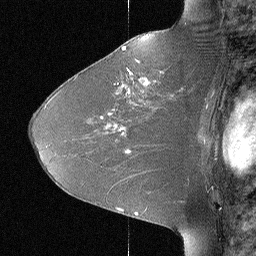
Breast MRI (dynamic contrast-enhanced), one sagittal slice; position 41 of 64 along the scan axis; dynamic contrast-enhanced study with each time point stored as its own series, time point 2 of 3 at this slice position (early post-contrast, ordered by acquisition time); 1.5 T; TE 4 ms, TR 30 ms; 2.25 mm slice thickness; 256 × 256 image matrix, field of view 180 × 180 mm. Patient: female, 46 years. From the clinical record (not read from this slice): setting: breast cancer imaged before/during neoadjuvant chemotherapy; receptor status: HR-positive, HER2-negative.
Outlined on this slice (semi-automatic segmentation, software-assisted and operator-edited):
- analysis volume of interest (the breast-tissue region the enhancement analysis was run in; not a lesion): box from (x=106, y=43) to (x=184, y=119) px
- tumour enhancement mask (voxels above the 90 % enhancement threshold inside the analysis volume of interest): (x=122, y=47)–(x=130, y=93)